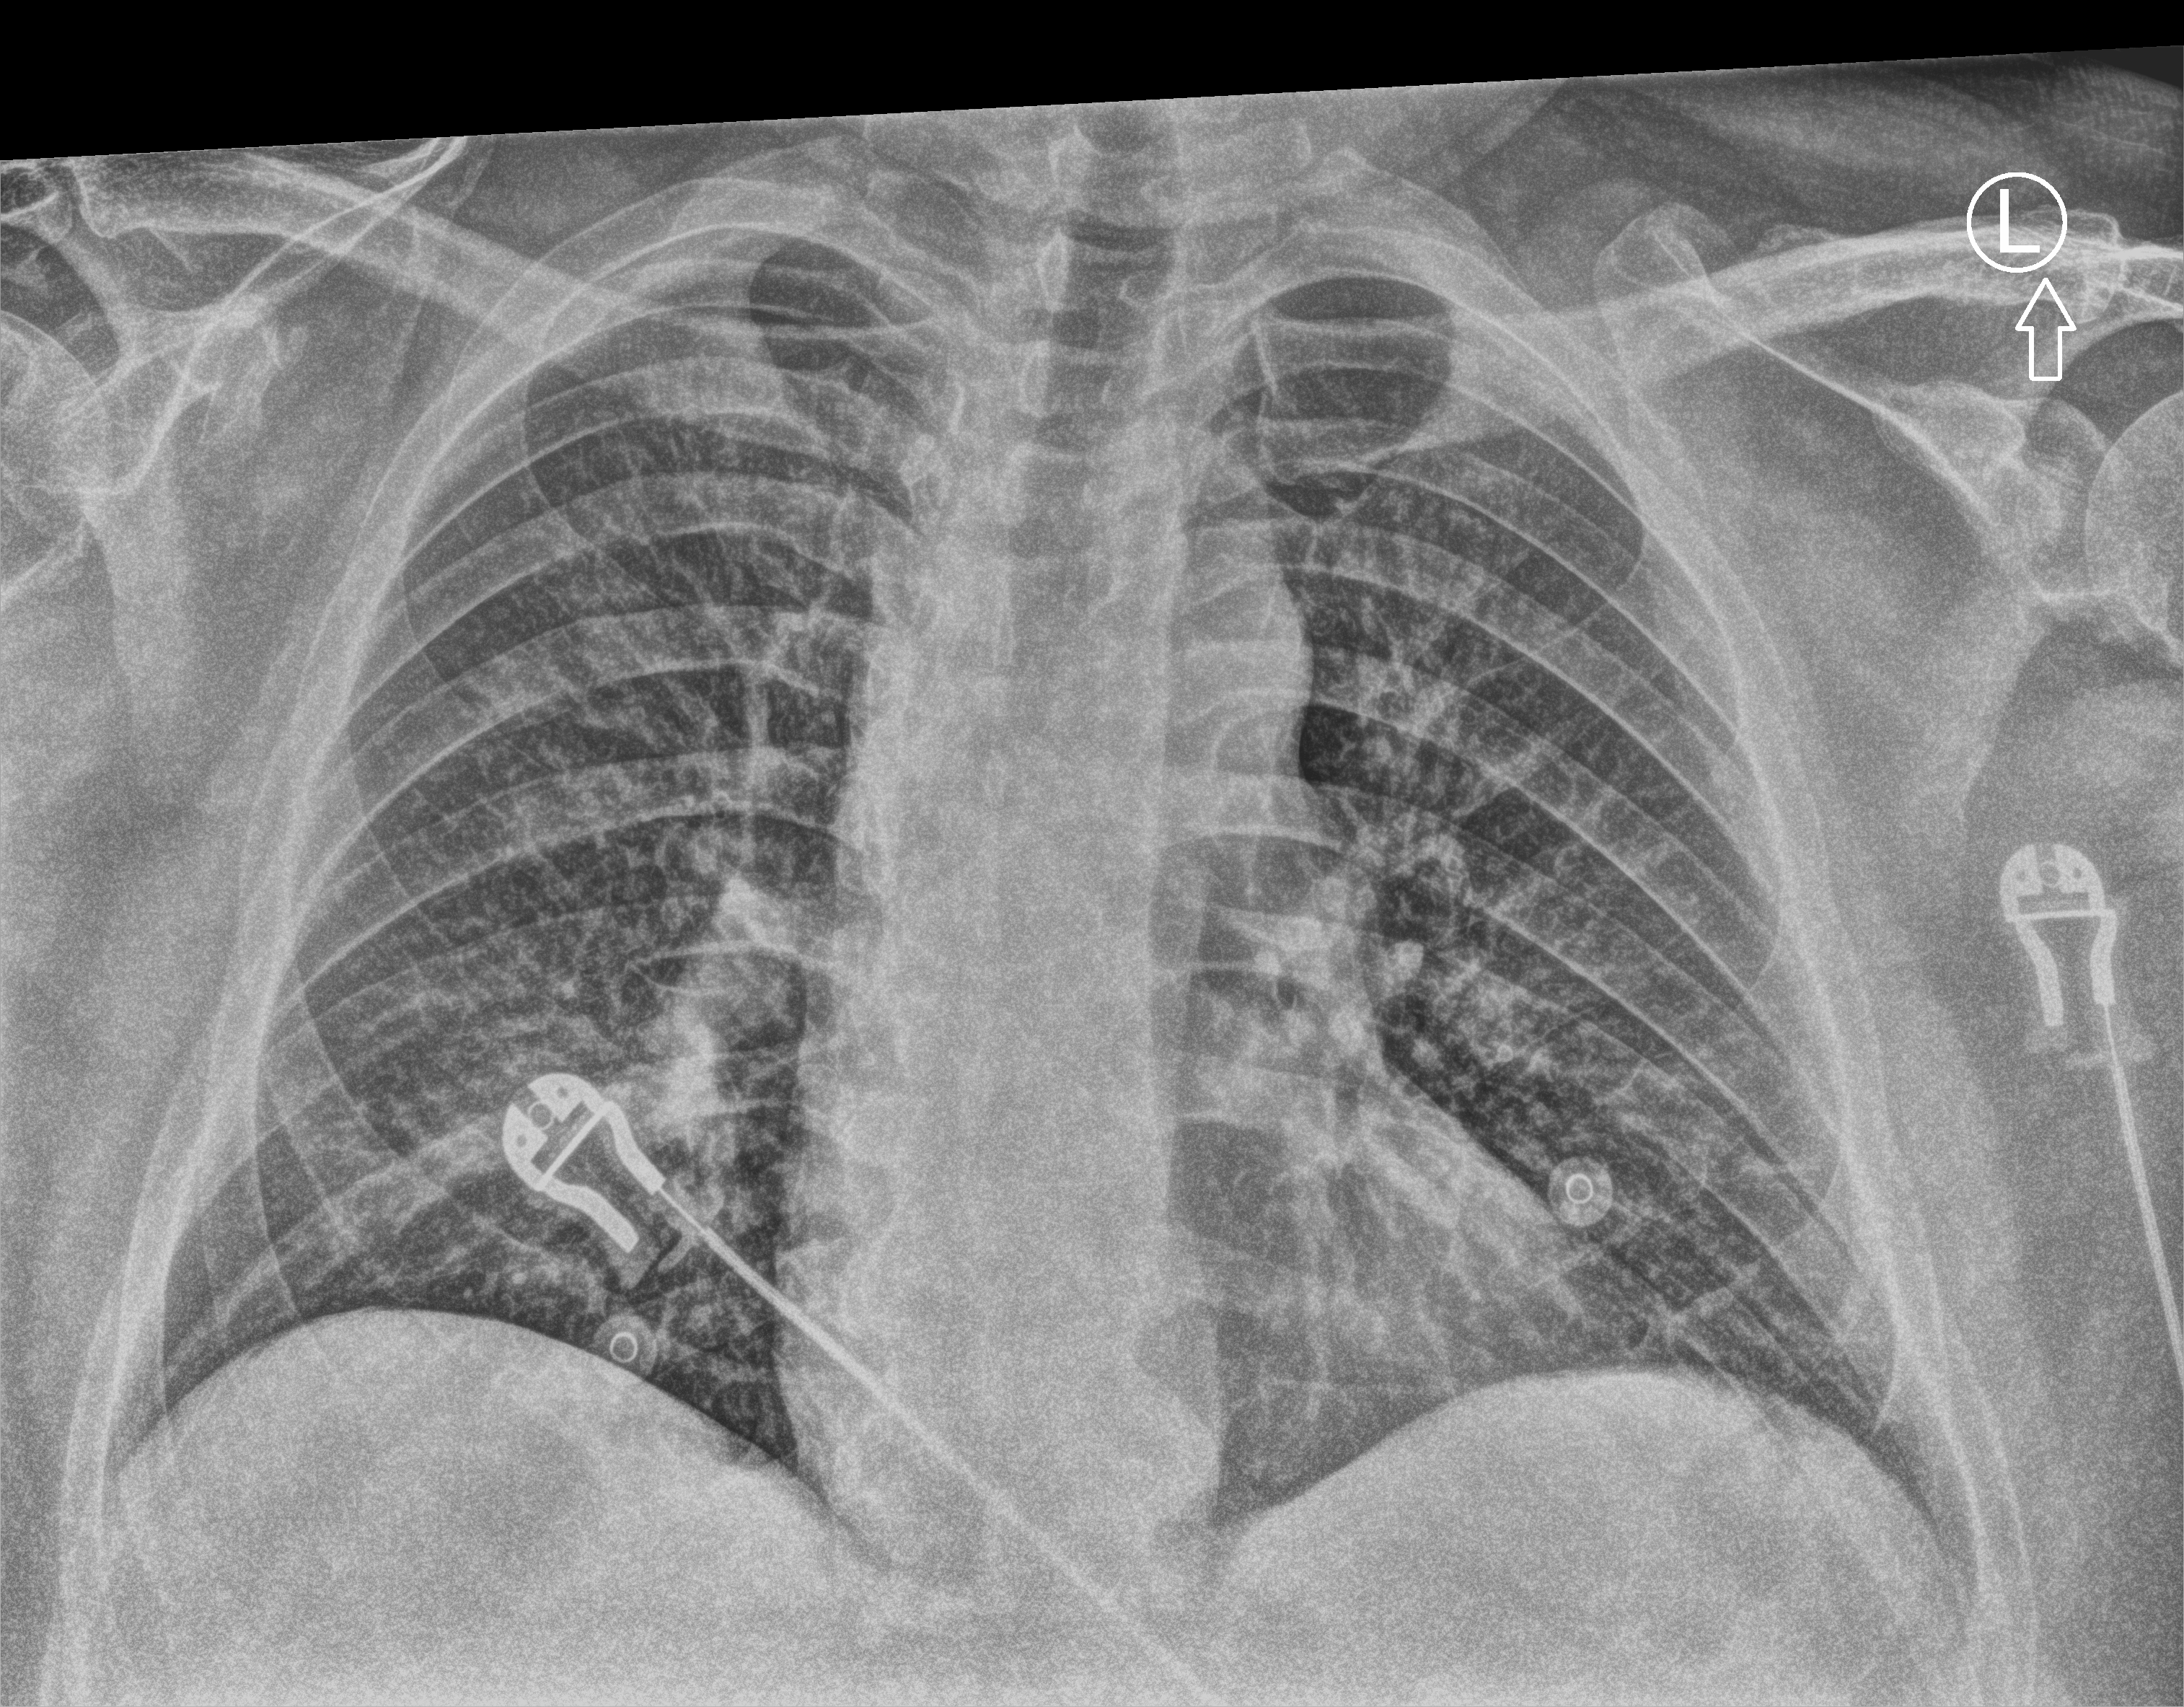
Bedside chest radiograph (computed radiography), anteroposterior (AP) projection. Male patient hospitalised with COVID-19, age 18–59 years.
From the hospital-stay record, not from the radiograph (when in the stay this image was taken is not recorded): admitted to intensive care during this hospital stay: no; mechanically ventilated during this hospital stay: no; length of hospital stay: 25 days.